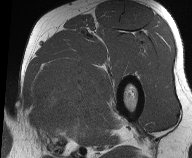
MRI of an extremity soft-tissue mass, one axial slice. Position 40 of 61 along the scan axis. MR volume resampled by the dataset authors to the PET/CT grid (not the native acquisition matrix). 192 × 158 image matrix, field of view 187 × 154 mm. Male patient. From the clinical record (not read from this slice): histological type: pleiomorphic liposarcoma; grade: high; site of the primary tumour: left thigh.
Outlined on this slice (expert contour drawn on MRI and transferred to this co-registered scan by the dataset authors):
- gross tumour volume including surrounding oedema: box from (x=30, y=60) to (x=101, y=138) px
- gross tumour volume (mass): (x=32, y=69)–(x=92, y=122)